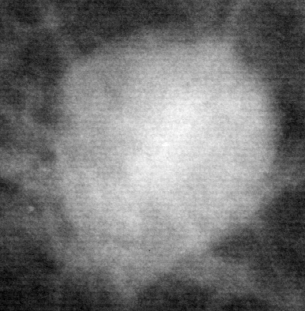
Crop from a digitized film mammogram around one marked abnormality; right breast; CC view.
- Finding: mass, shape oval, margins microlobulated; BI-RADS assessment category 4; pathology result (as recorded, not read from the image): malignant.